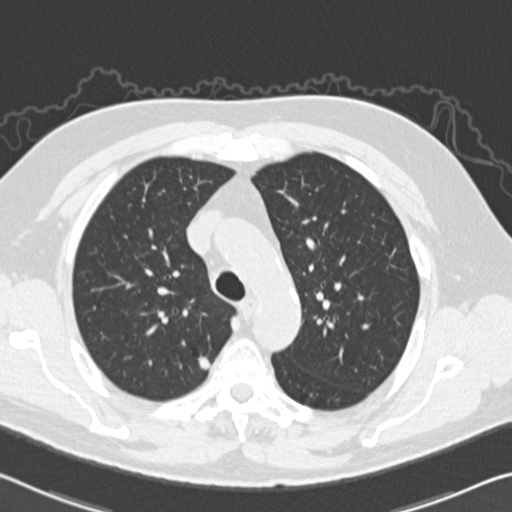
Low-dose screening chest CT, one axial slice; 120 kVp; lung window (W 1500 / L -600 HU); 2 mm slice thickness; 512 × 512 image matrix, field of view 340 × 340 mm.
Outlined on this slice (outlined manually by an expert reader):
- lesion 1 (tumor, upper lobe of right lung): bounding box <198,356,210,370> (left, top, right, bottom; pixels)